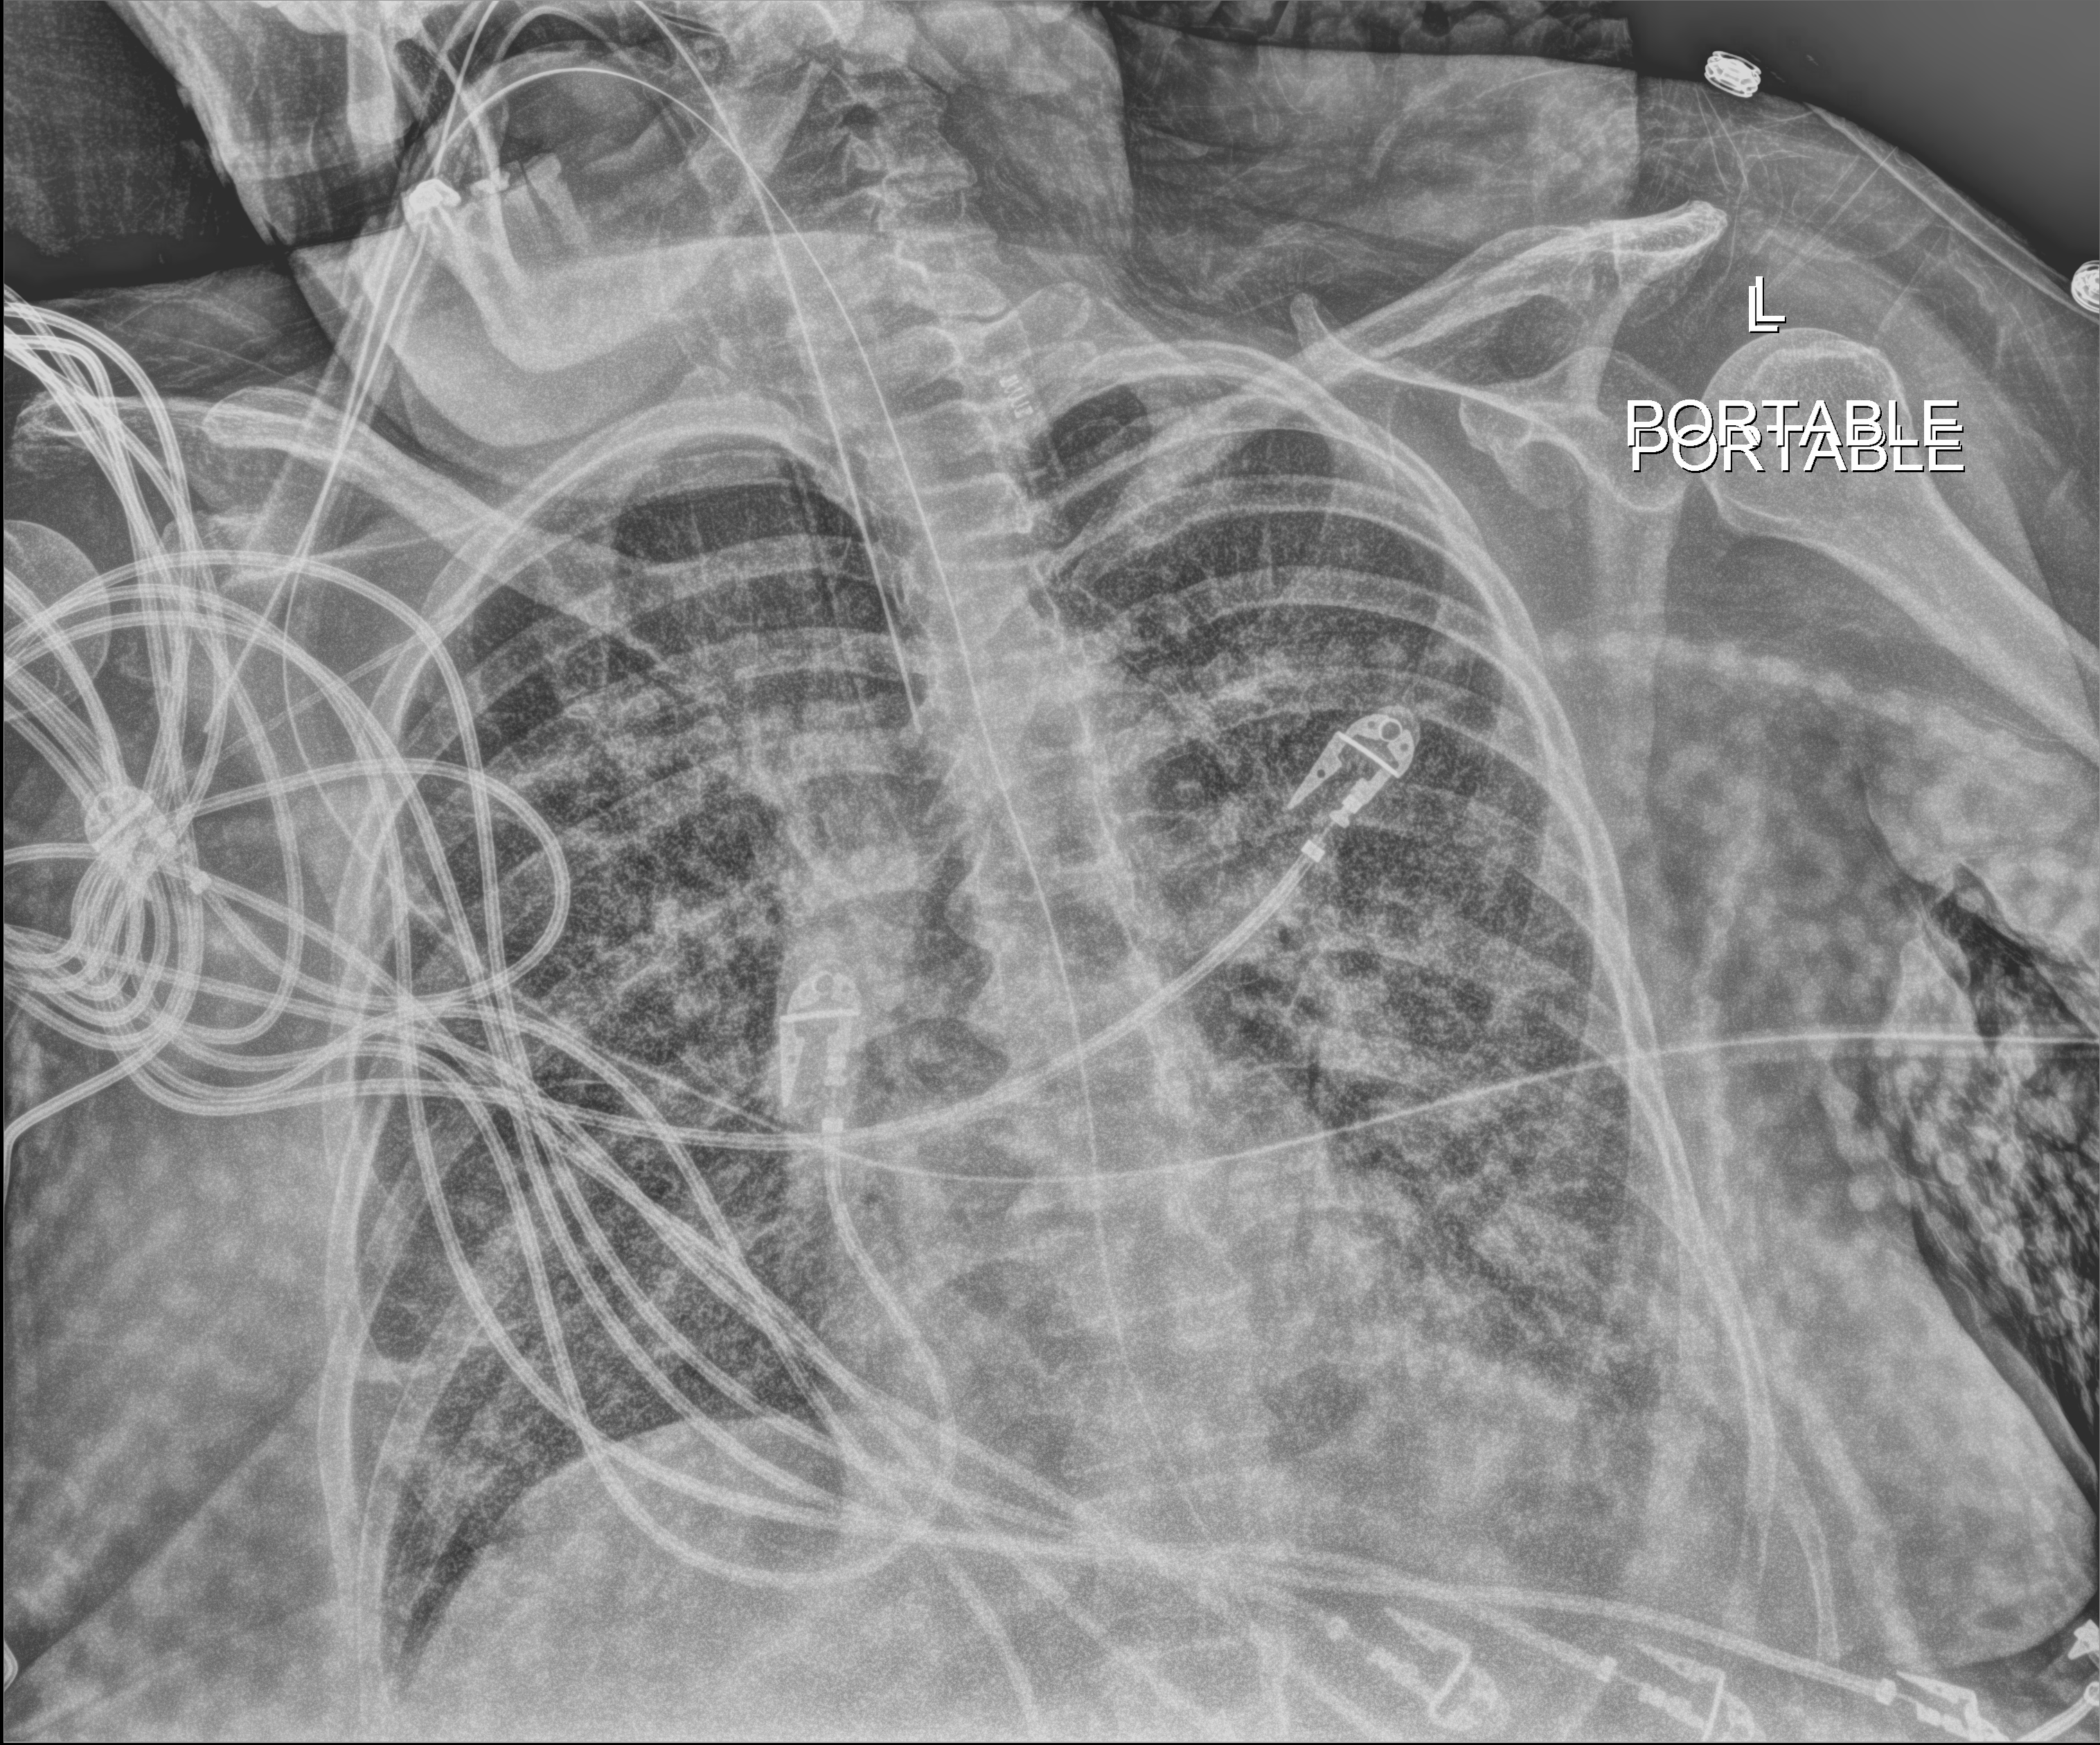
Bedside chest radiograph (digital radiography). Female patient hospitalised with COVID-19, age 60–74 years.
From the hospital-stay record, not from the radiograph (when in the stay this image was taken is not recorded): length of hospital stay: 38 days.